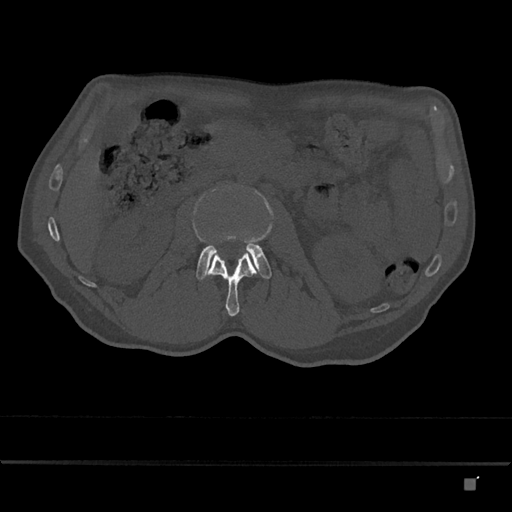
CT including the spine, one axial slice; reconstruction kernel Br40s/3; bone window (W 1800 / L 400 HU); 0.5 mm slice thickness; 512 × 512 image matrix, field of view 390 × 390 mm. Patient: male, 72 years. Case-level facts recorded for this patient, not image findings: primary cancer: prostate.
Annotated regions visible in this slice (semi-automatically segmented with operator editing):
- L2 vertebra: bounding box [x1, y1, x2, y2] px = [205, 251, 257, 317]
- L3 vertebra: [196, 243, 272, 280]